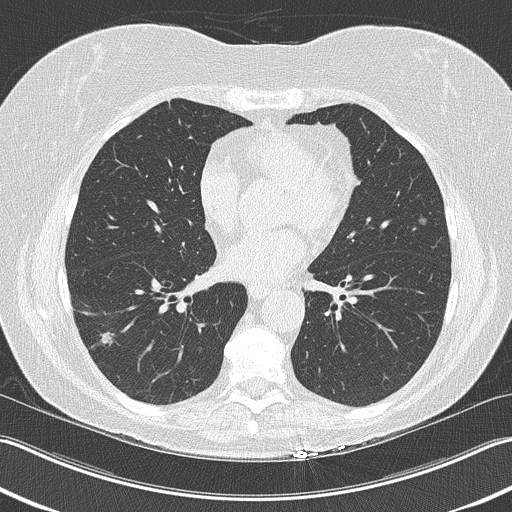
Low-dose screening chest CT, one axial slice. Position 104 of 210 along the scan axis. Reconstruction kernel B50f. Lung window (W 1500 / L -600 HU). 512 × 512 image matrix.
Outlined on this slice (outlined manually by an expert reader):
- lesion 1 (tumor, lower lobe of right lung): bounding box <100,332,114,346> (left, top, right, bottom; pixels)